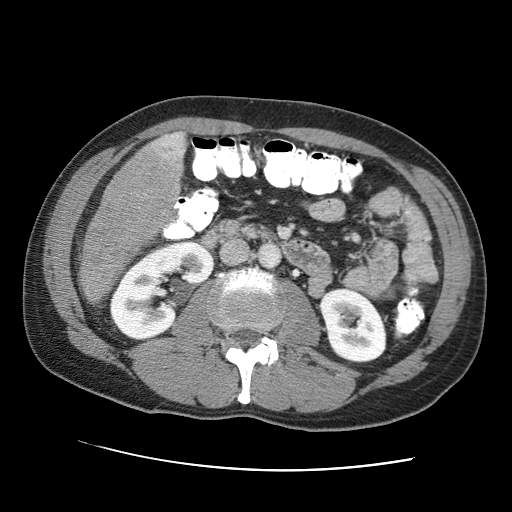
Contrast-enhanced abdominal CT (liver protocol), one axial slice. Slice 18 of 95 in the series (ordered by position). Reconstruction kernel STANDARD. 120 kVp. One of 2 acquisitions stored at this slice position. Soft-tissue window (W 400 / L 40 HU). 512 × 512 image matrix, field of view 360 × 360 mm. From the clinical record (not read from this slice): diagnosis: hepatocellular carcinoma (patient treated with transarterial chemoembolisation; whether this scan precedes or follows treatment is not stated here); TNM stage (as recorded): Stage-IVA; Child-Pugh class: A; tumour nodularity: multinodular.
Structures marked on this image (semi-automatic segmentation, software-assisted and operator-edited):
- liver parenchyma outside the tumour (the mass and vessels are separate outlines, so this box may not span the whole liver): bounding box [x1, y1, x2, y2] px = [116, 132, 186, 222]
- mass: [78, 133, 183, 305]